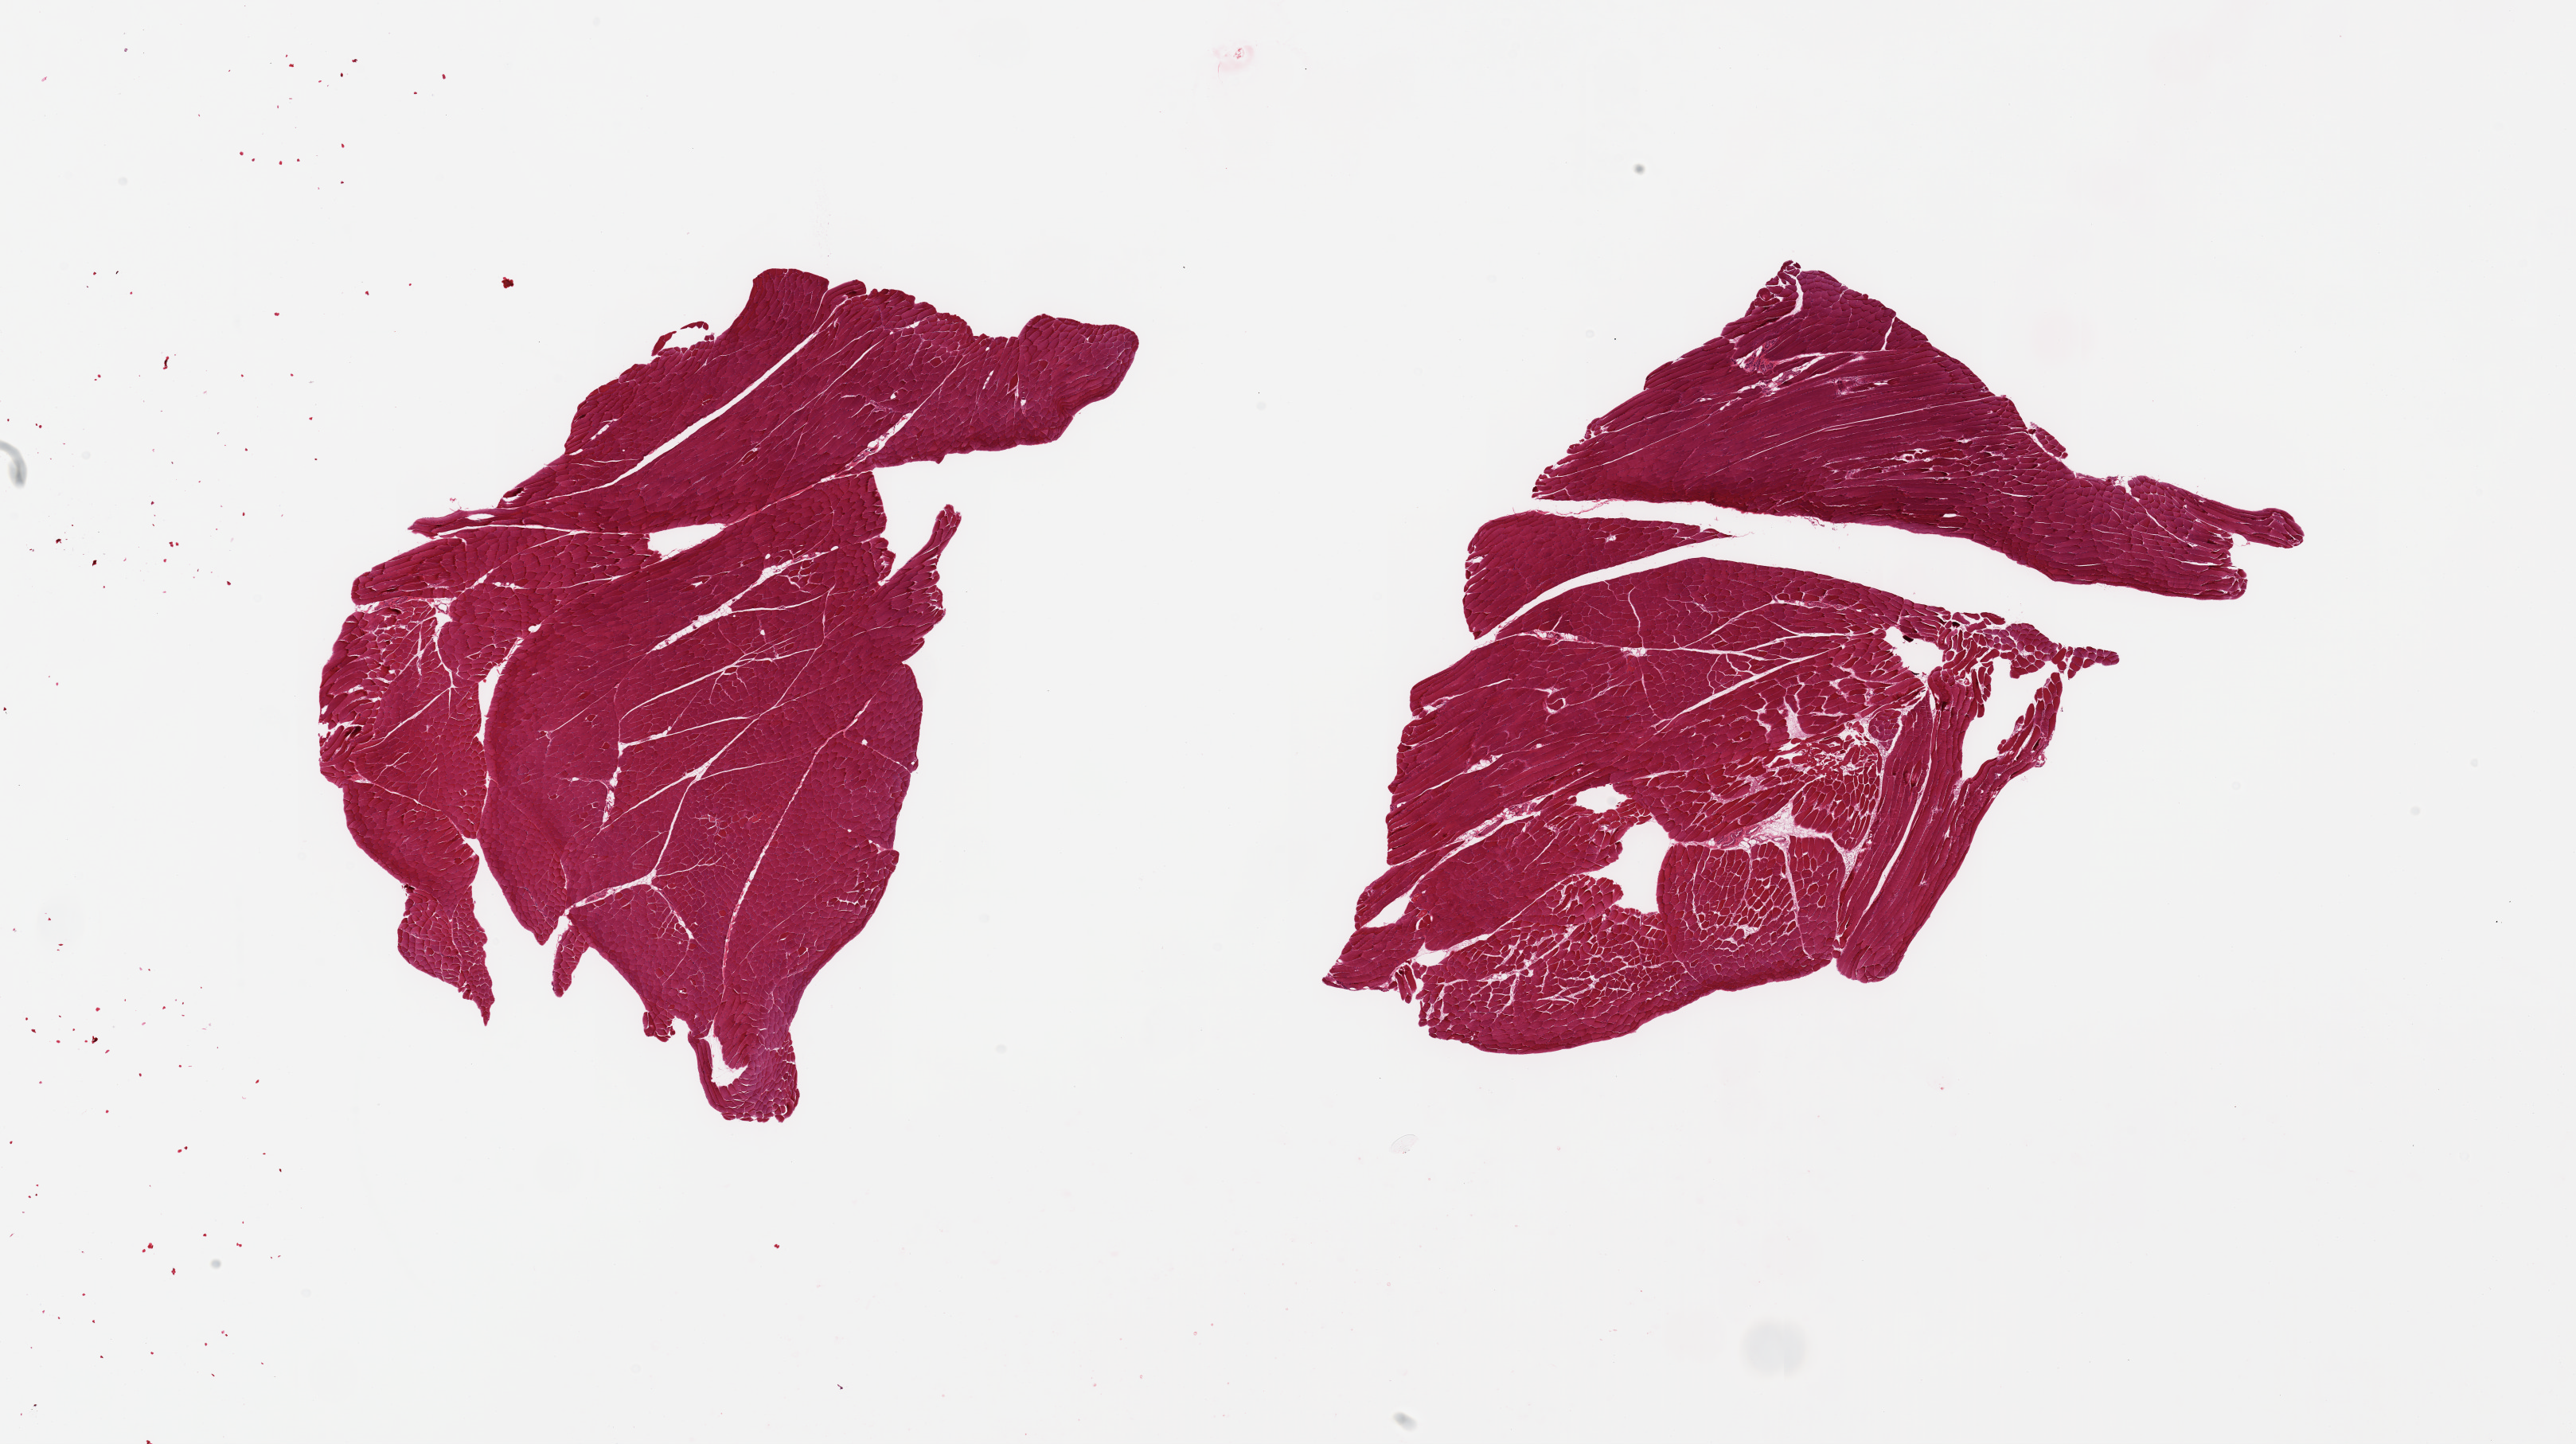
Haematoxylin and eosin whole-slide image, shown as a low-resolution overview of the whole scanned area (about 25.6 x 14.3 mm, slide scanned at 20x); PAXgene-fixed paraffin-embedded (PFPE) section; sampled site (target tissue): skeletal muscle; donor tissue sample. Donor: female.
Pathologist's review note for this sample: 2 pieces; no fat.